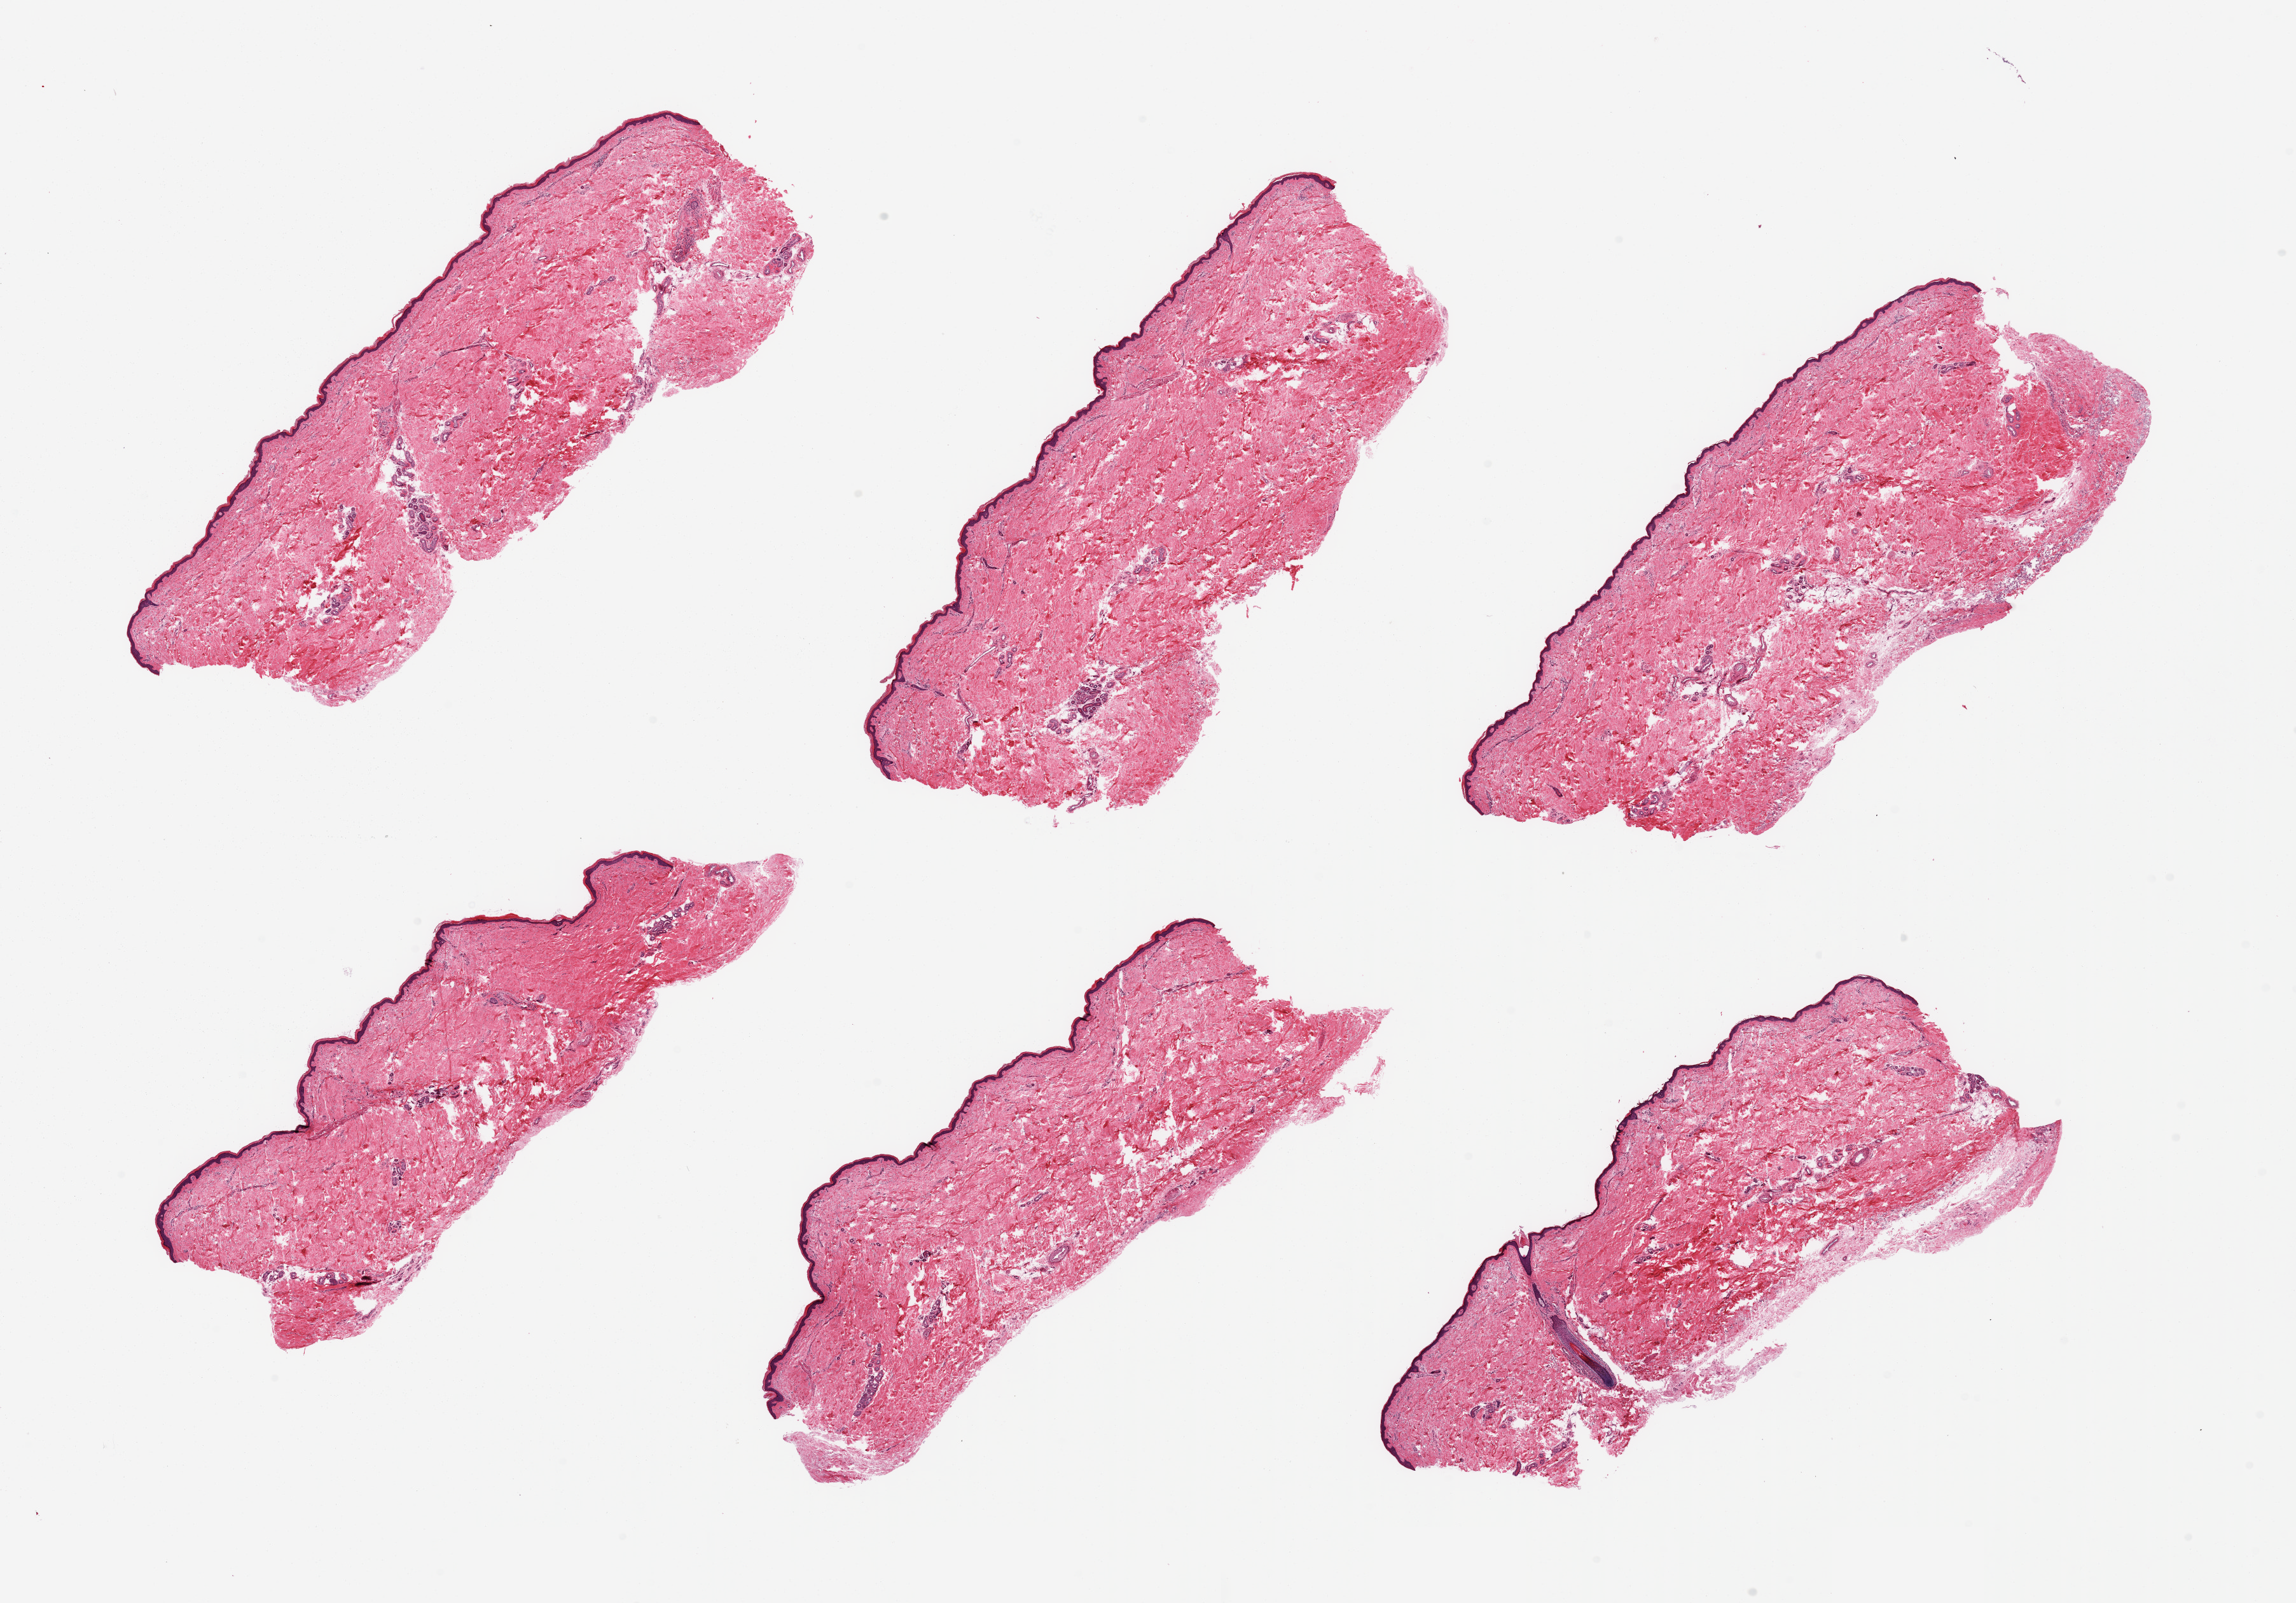
Haematoxylin and eosin whole-slide image, brightfield — a low-resolution overview of the entire scanned area, about 28.5 x 19.9 mm, PAXgene-fixed paraffin-embedded (PFPE) section, target tissue: skin of lower leg, donor tissue sample. Donor sex: male.
Reviewer comment on this tissue sample: 6 pieces; well trimmed; minimal dermal fat.